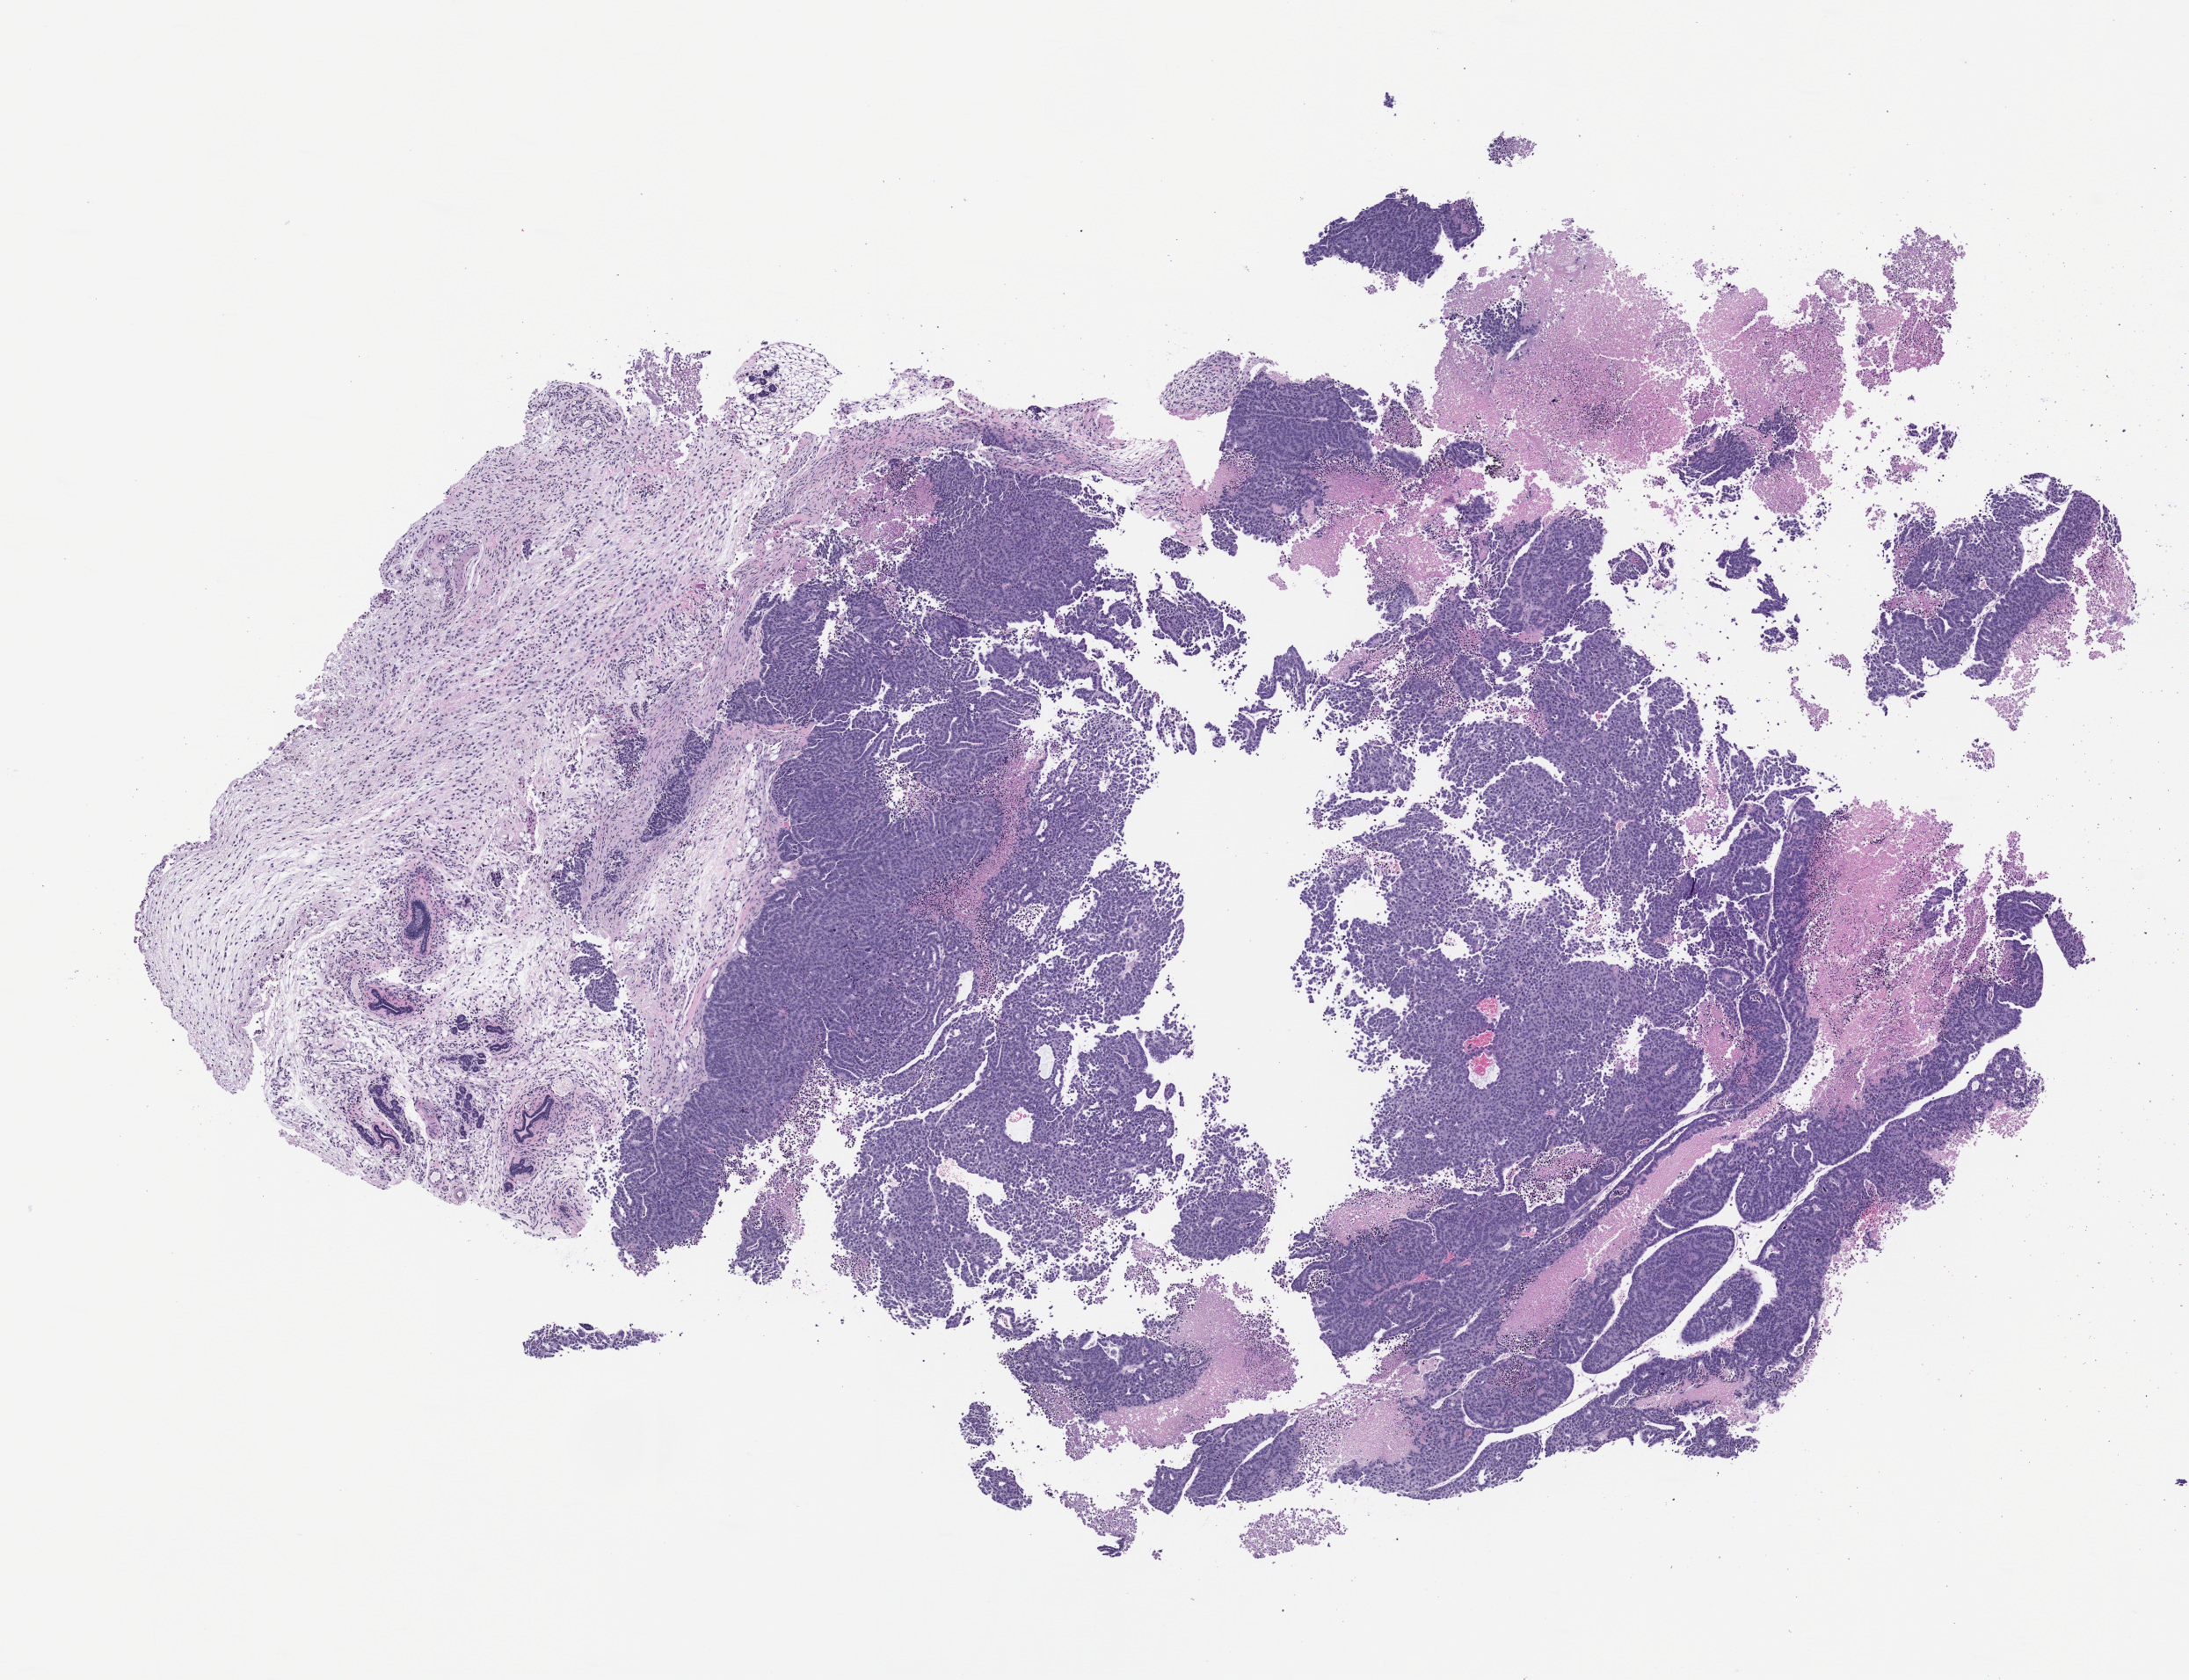
Whole-slide image, haematoxylin and eosin: patient-derived xenograft (human tumor grown in a mouse), passage 1, low-resolution overview of the scanned area, about 10.0 x 7.7 mm, FFPE section, tumor site category: colon.
- originating patient diagnosis: Colon Adenocarcinoma